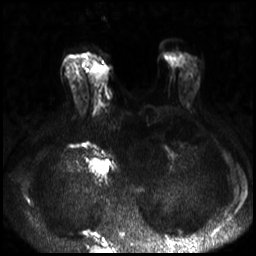
Breast MRI, one axial slice. Position 9 of 30 along the scan axis. Diffusion-weighted series; image 2 of 4 stored at this slice position (different b-values; order by instance number). 3 T. 4 mm slice thickness. 256 × 256 image matrix, field of view 320 × 320 mm. Female patient.
Structures marked on this image (expert manual segmentation):
- tumour on diffusion-weighted imaging: bounding box (x1, y1, x2, y2) in pixels: (91, 65, 108, 85)